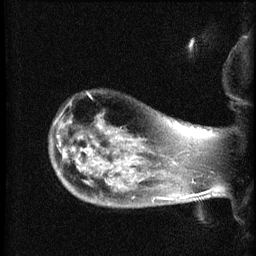
Breast MRI (dynamic contrast-enhanced), one sagittal slice. Position 55 of 60 along the scan axis. Dynamic contrast-enhanced series, image 2 of 3 at this slice position (ordered by acquisition). 1.5 T. TE 4.2 ms, TR 8.2 ms. 2.1 mm slice thickness. 256 × 256 image matrix, field of view 180 × 180 mm. Female patient, age 50 years.
Outlined on this slice (semi-automatically segmented with operator editing):
- analysis volume of interest (the breast-tissue region the enhancement analysis was run in; not a lesion): box from (x=50, y=111) to (x=169, y=207) px
- tumour enhancement mask (voxels above the 70 % enhancement threshold inside the analysis volume of interest): (x=161, y=197)–(x=164, y=199)